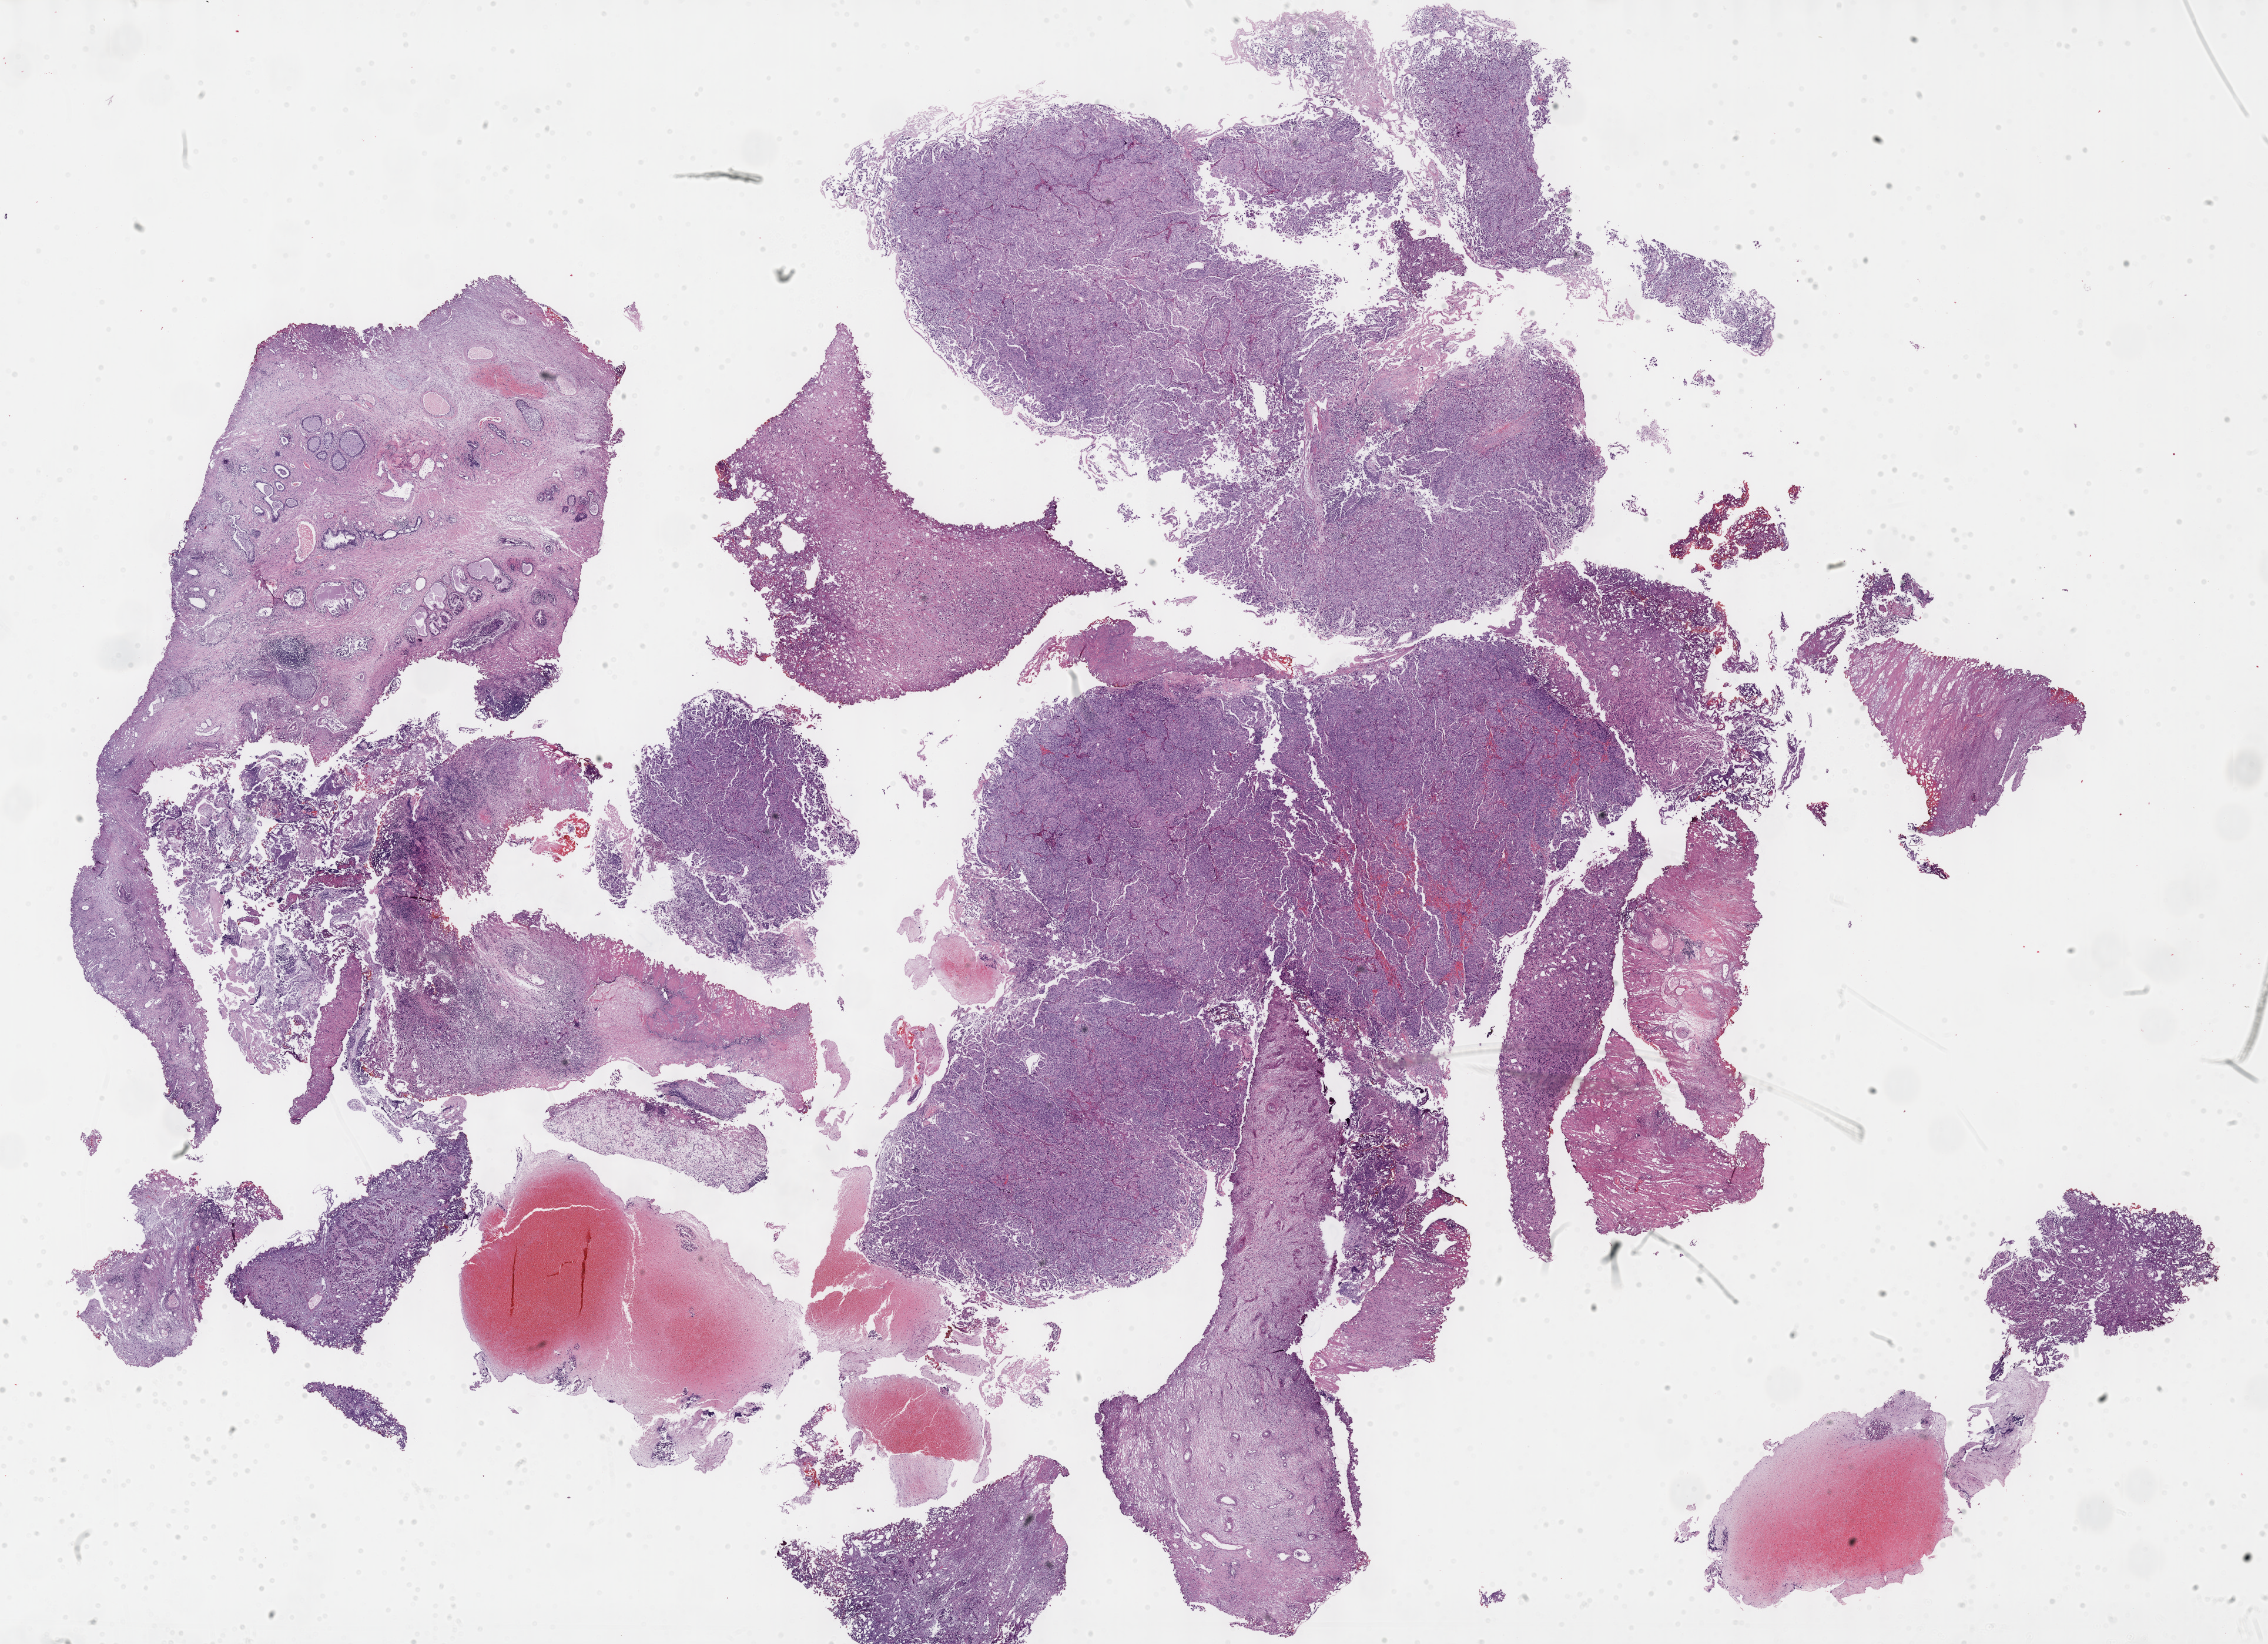
H&E whole-slide image — shown as a low-resolution overview of the whole scanned area (about 31.2 x 22.6 mm, slide scanned at 40x); formalin-fixed paraffin-embedded (FFPE) diagnostic section; sample: primary tumour, bladder. Patient: male, age at initial diagnosis 77 years. Histologic grade: high grade.
Diagnosis: Transitional cell carcinoma. TNM: T3 N1 M0. AJCC pathologic stage: IV (7th edition).